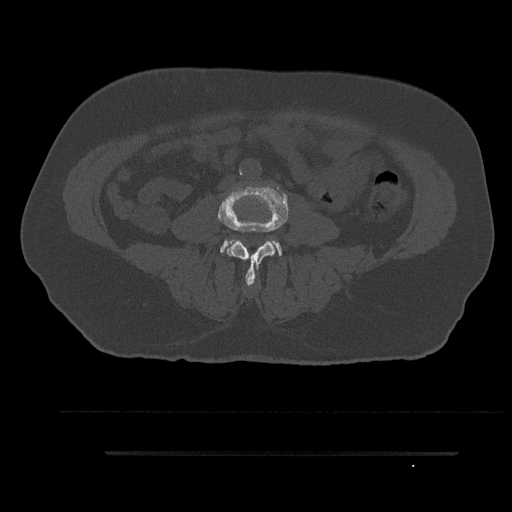
CT including the spine, one axial slice. Slice 15 of 797 in the series (ordered by position). Bone window (W 1800 / L 400 HU). 512 × 512 image matrix. Patient: male, 63 years. From the clinical record (not read from this slice): primary cancer: renal.
Structures marked on this image (semi-automatic segmentation, software-assisted and operator-edited):
- L3 vertebra: bounding box (x1, y1, x2, y2) in pixels: (218, 186, 289, 286)
- L4 vertebra: (220, 238, 282, 256)